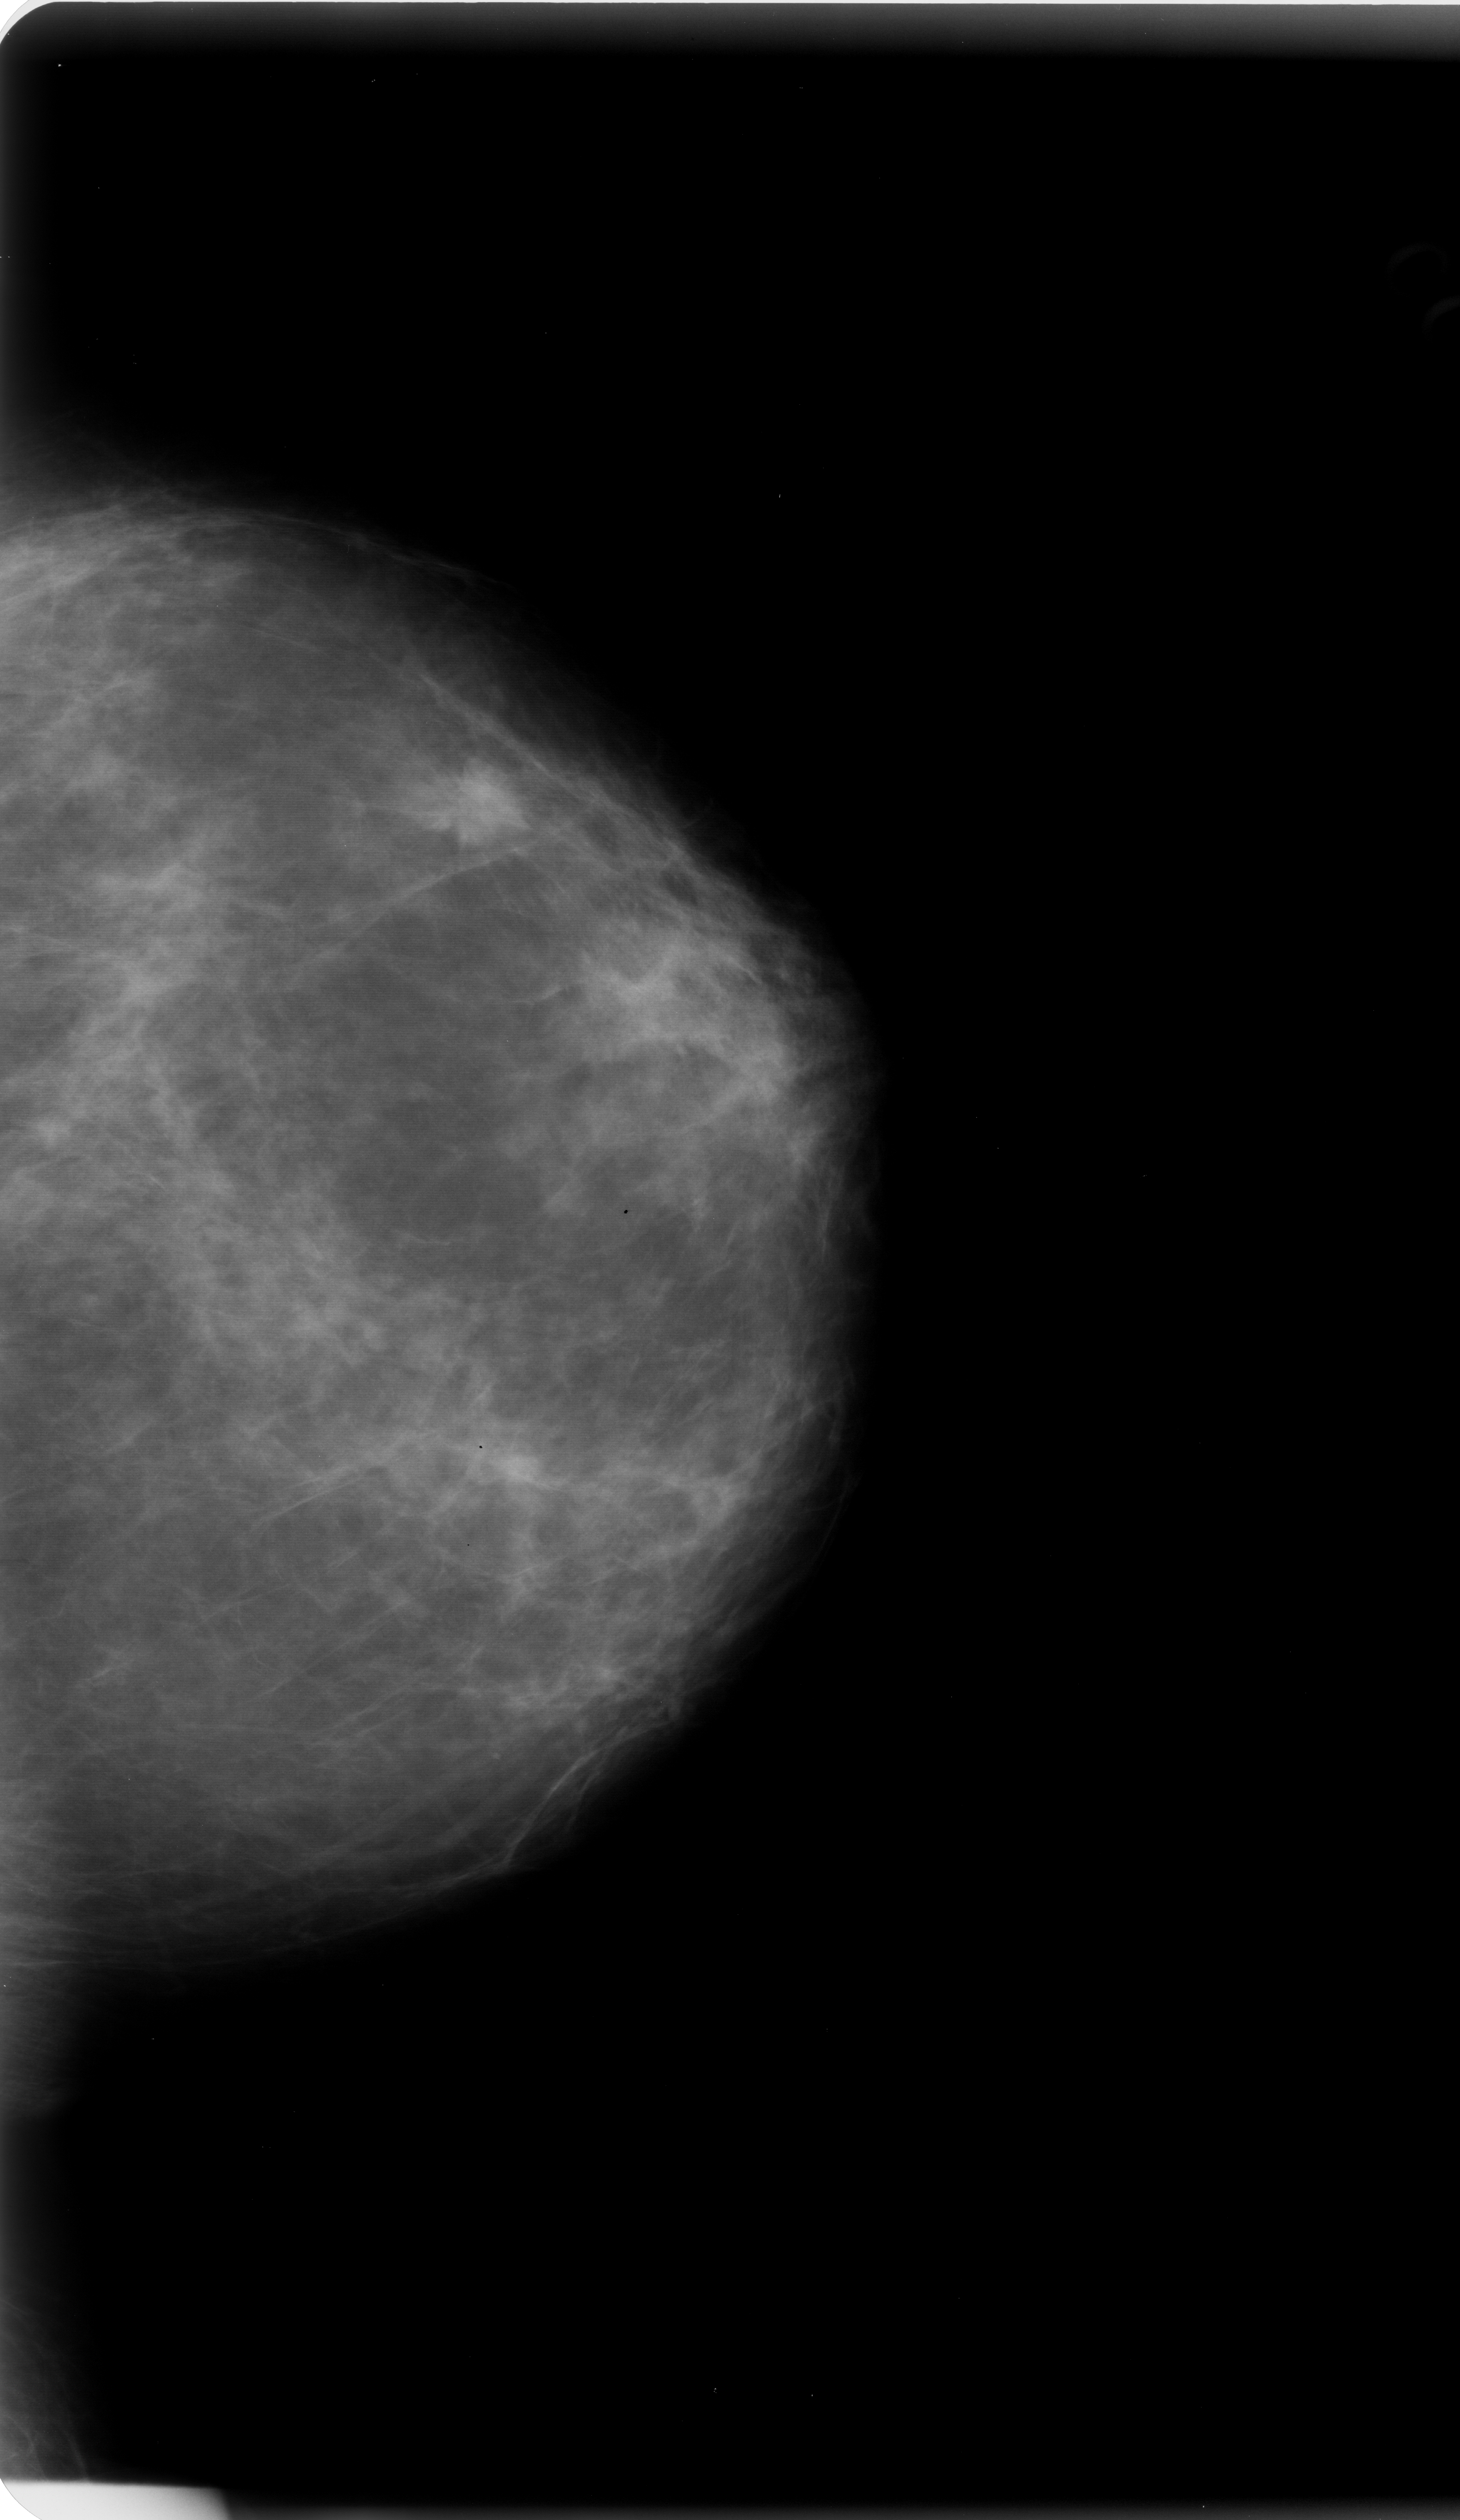
Mammogram (digitized film); left breast; CC view; BI-RADS breast density category 2 (scale 1–4).
Mass, shape round, margins spiculated; BI-RADS assessment category 5; pathology (as recorded): malignant.